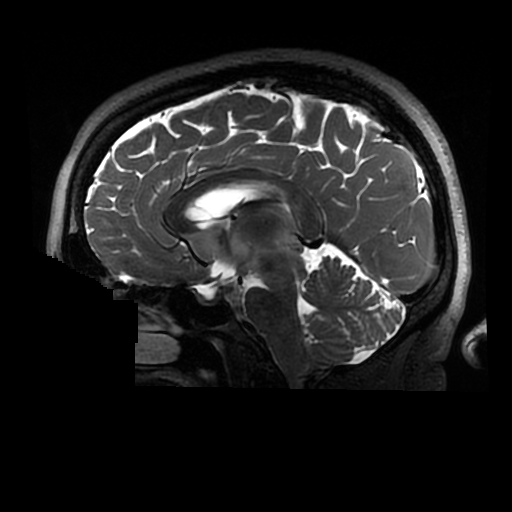
Brain MRI from a brain-tumour surgery series, one sagittal slice. Slice 152 of 320 in the series (ordered by position). 0.6 mm slice thickness. 512 × 512 image matrix, field of view 240 × 240 mm. From the clinical record (not read from this slice): histopathology: Astrocytoma; WHO grade: 2; IDH mutation: yes.
Outlined on this slice (outlined manually by an expert reader):
- tumour: bounding box (x1, y1, x2, y2) in pixels: (276, 209, 295, 244)